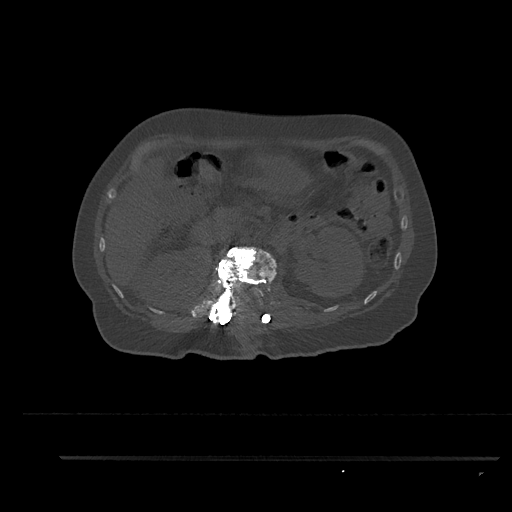
CT including the spine, one axial slice; position 215 of 797 along the scan axis; 120 kVp; bone window (W 1800 / L 400 HU); 0.5 mm slice thickness; 512 × 512 image matrix. Female patient, age 44 years. Case-level facts recorded for this patient, not image findings: primary cancer: renal; vertebrae with lytic lesions (as recorded): L1.
Structures marked on this image (semi-automatically segmented with operator editing):
- L1 vertebra: bounding box (x1, y1, x2, y2) in pixels: (204, 246, 277, 321)